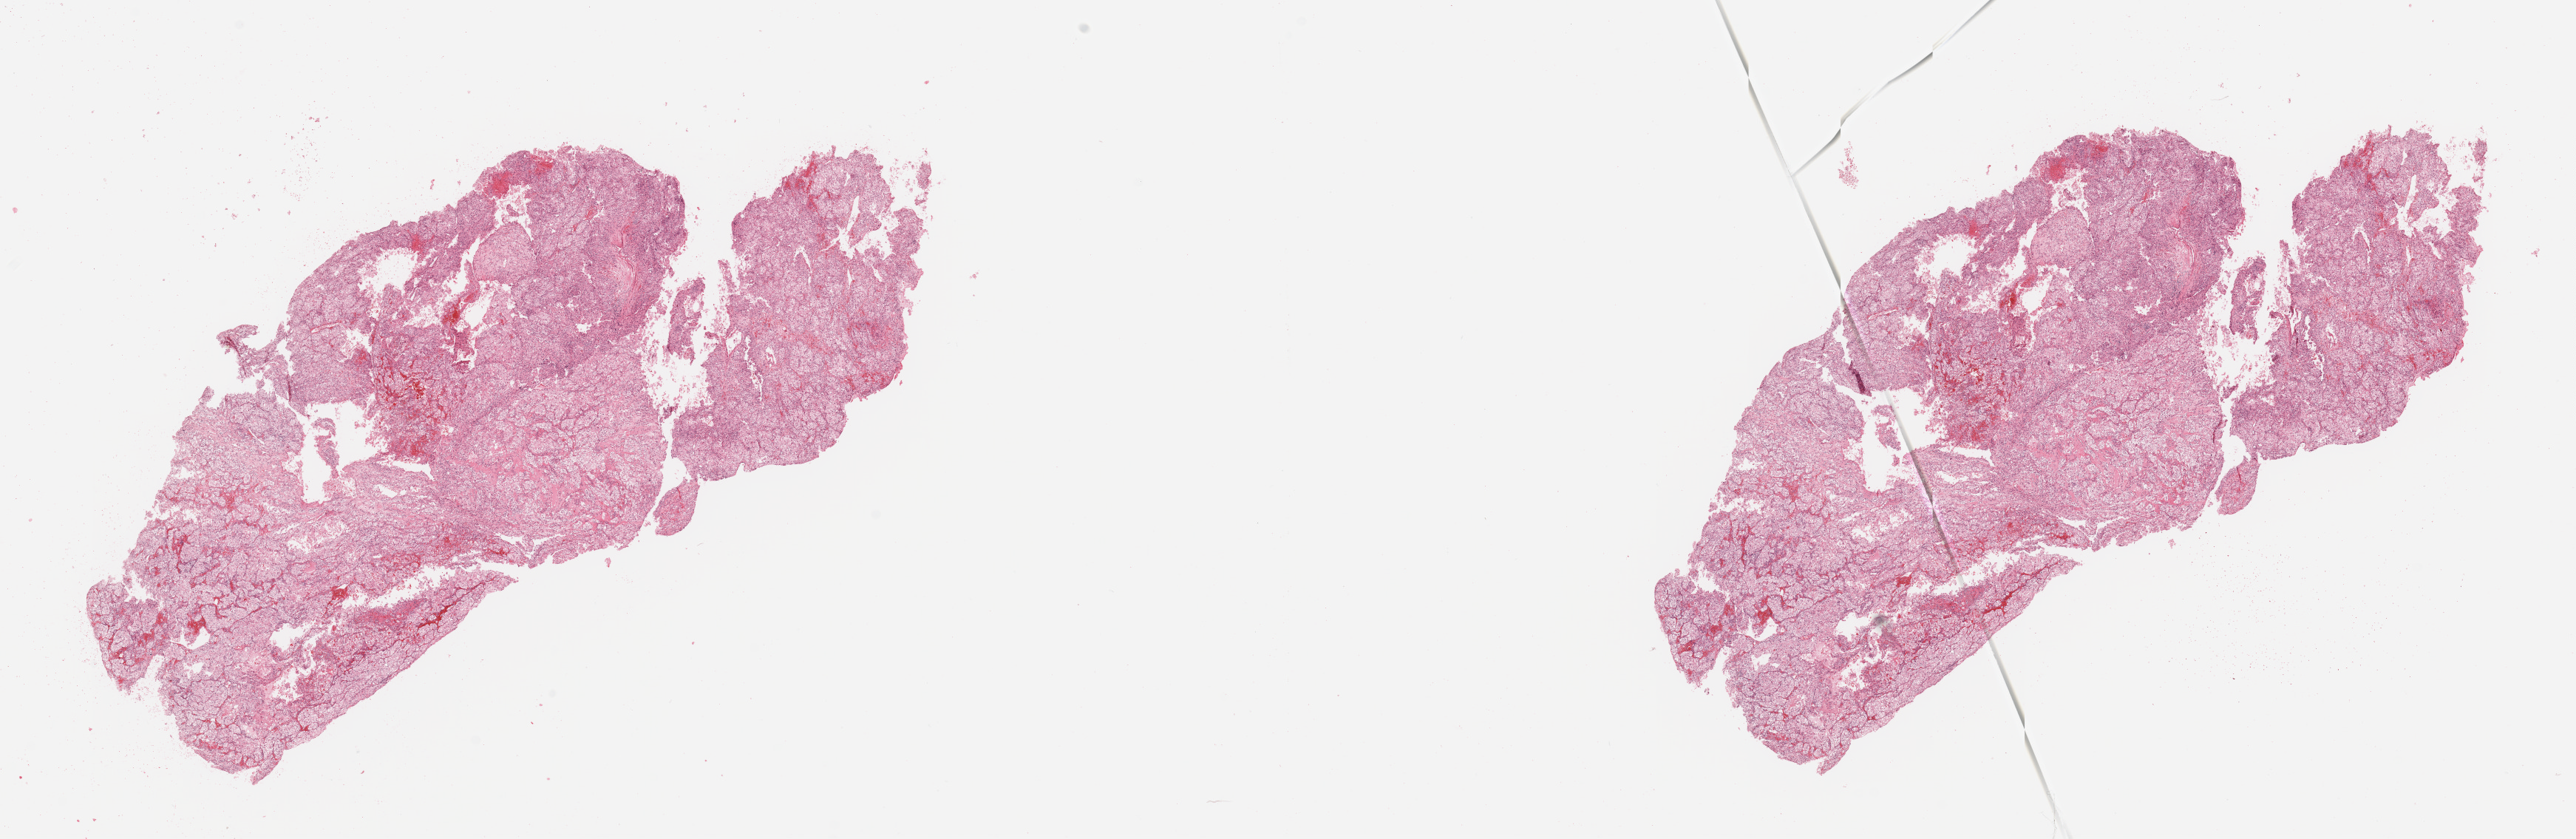
H&E whole-slide image, low-resolution overview of the scanned area, about 27.6 x 9.0 mm, tumour tissue sample, sampled site: kidney. Patient: male, age 56 years. Histologic grade: G2 (moderately differentiated). Composition of this section per pathologist review: tumour nuclei 80%, necrosis 10%.
AJCC pathologic stage: III. Diagnosis: Renal cell carcinoma, NOS.